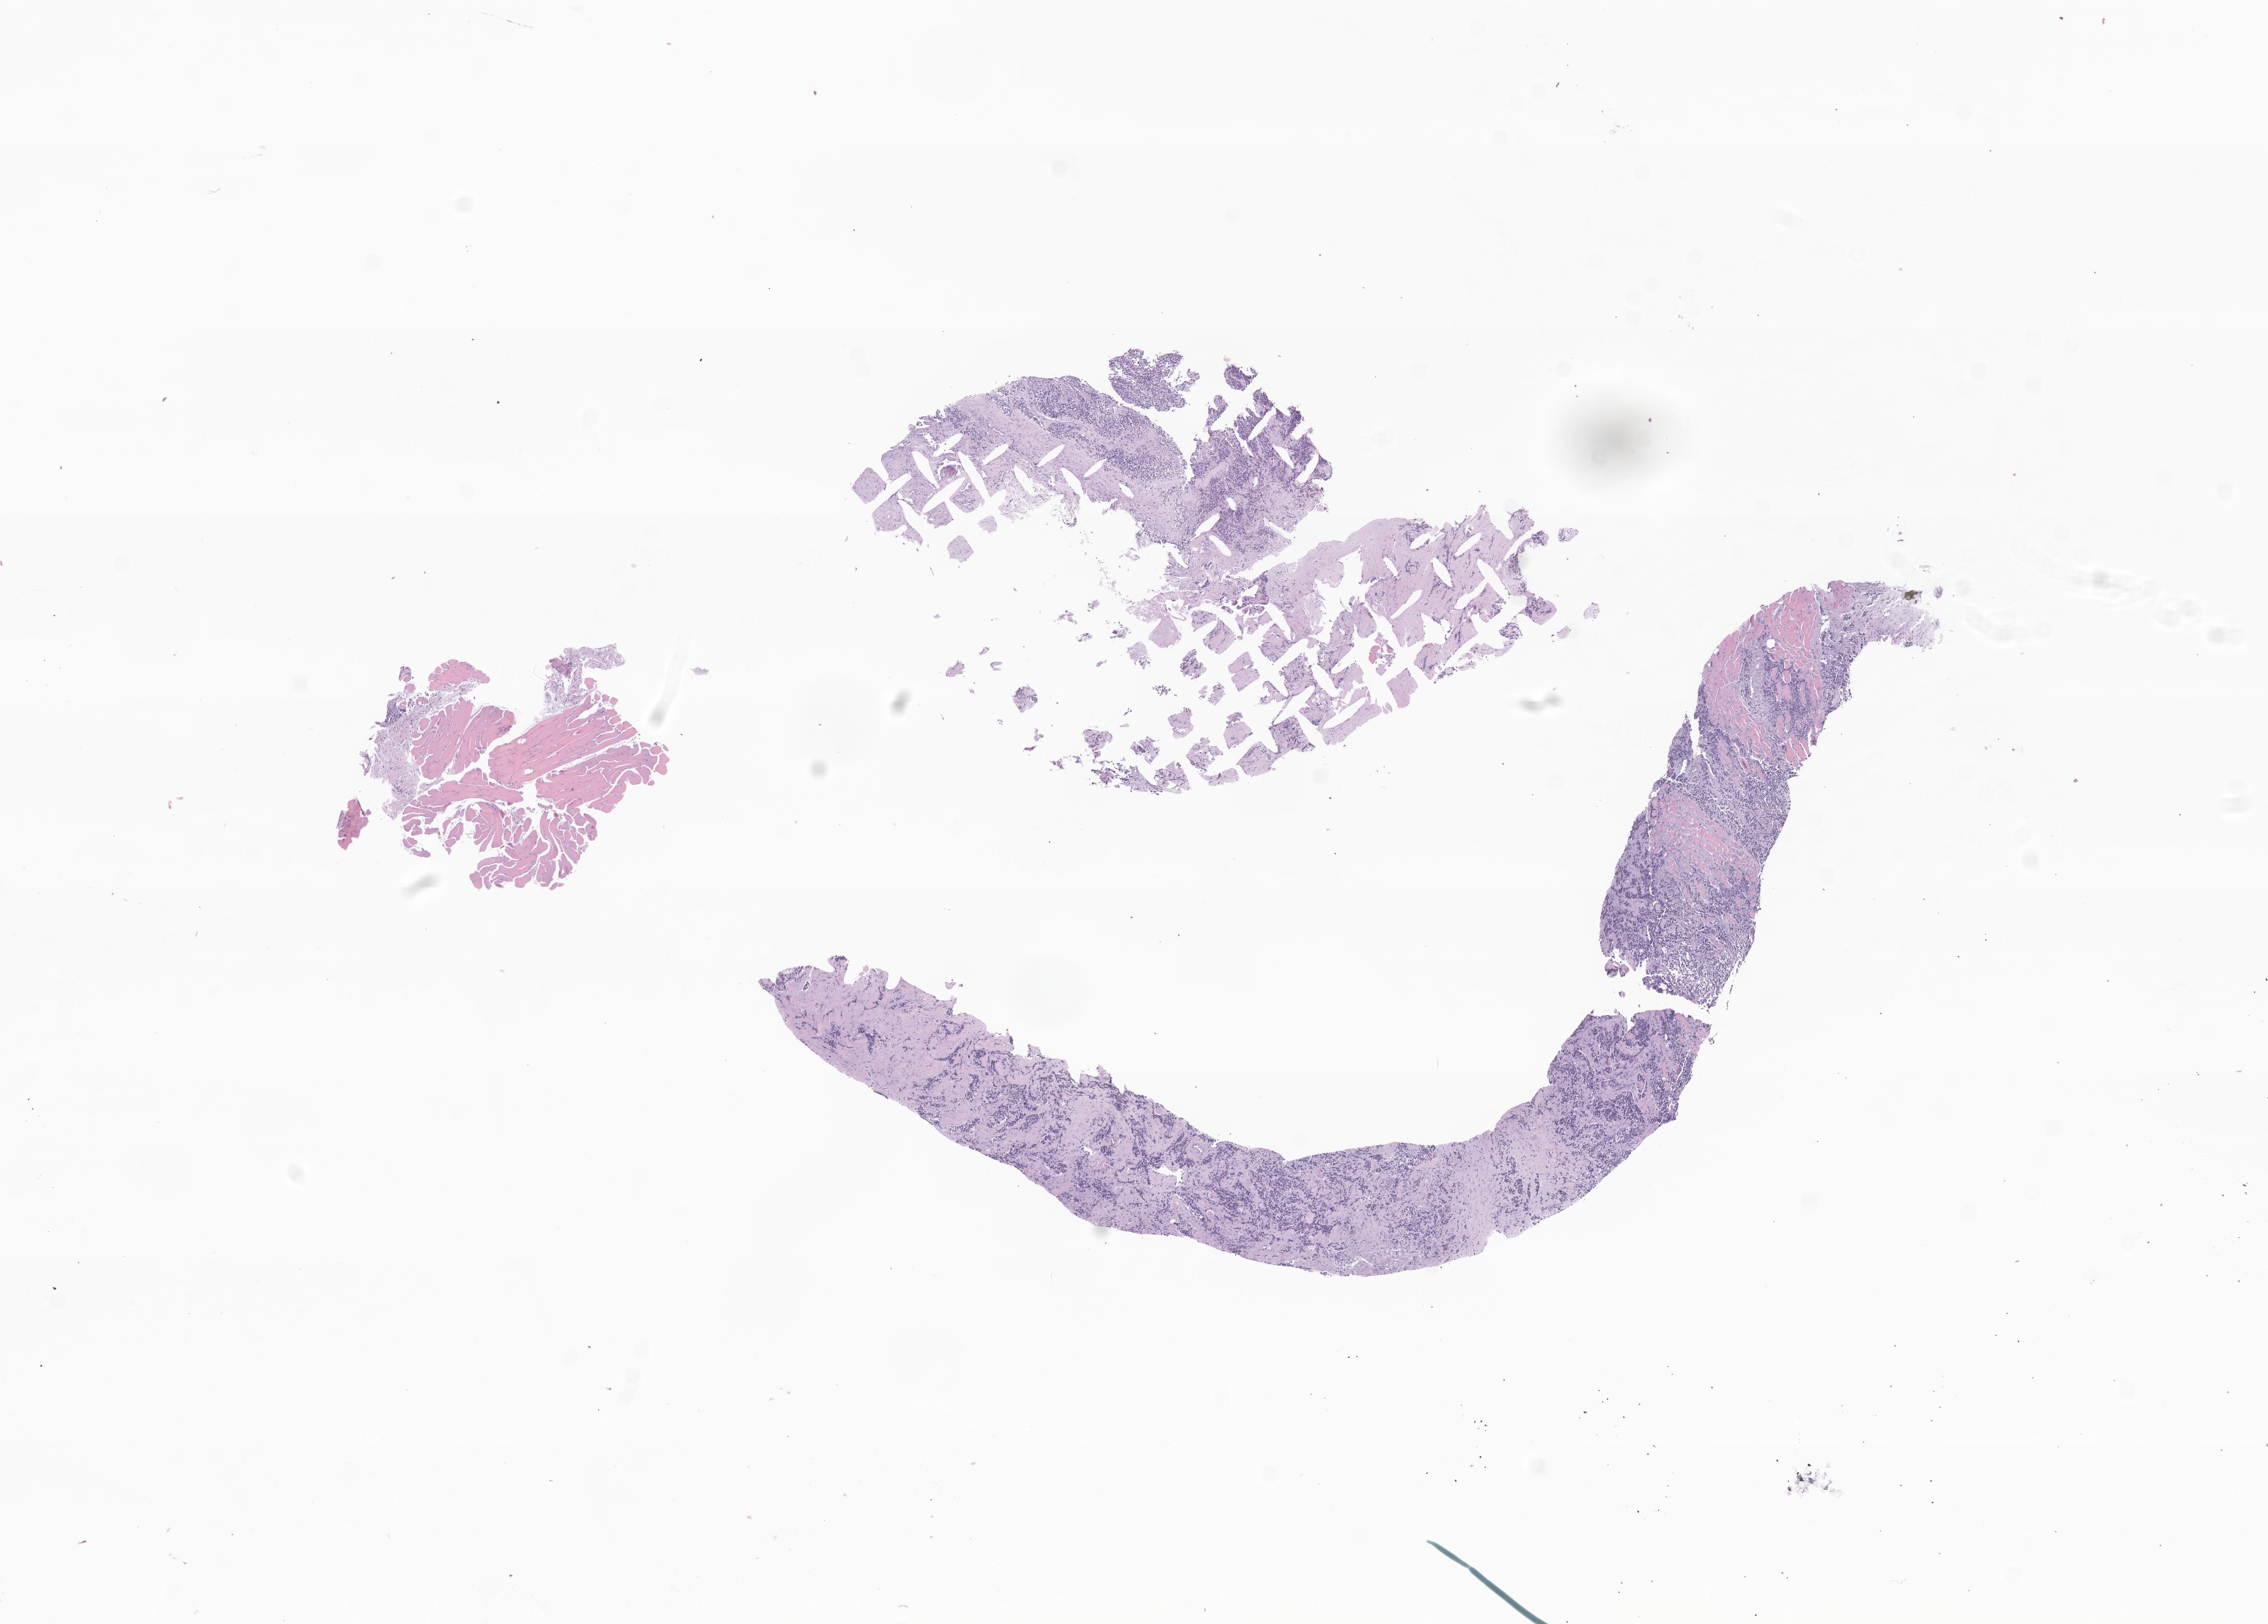
Haematoxylin and eosin whole-slide image of tumor tissue from the upper limb, low-resolution overview of the scanned area, about 13.0 x 9.3 mm. Formalin-fixed paraffin-embedded section. Patient: male, age 187 months.
Recorded diagnosis: Rhabdomyosarcoma, NOS.